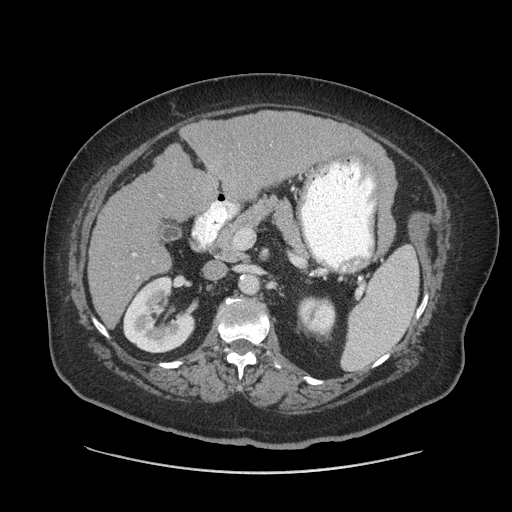
Contrast-enhanced abdominal CT (liver protocol), one axial slice. Slice 34 of 91 in the series (ordered by position). Soft-tissue window (W 400 / L 40 HU). 2.5 mm slice thickness. 512 × 512 image matrix. From the clinical record (not read from this slice): diagnosis: hepatocellular carcinoma (patient treated with transarterial chemoembolisation; whether this scan precedes or follows treatment is not stated here); TNM stage (as recorded): Stage-I; Child-Pugh class: A; tumour differentiation: well differentiated; tumour nodularity: uninodular.
Outlined on this slice (semi-automatic segmentation, software-assisted and operator-edited):
- liver parenchyma outside the tumour (the mass and vessels are separate outlines, so this box may not span the whole liver): bounding box <88,110,386,326> (left, top, right, bottom; pixels)